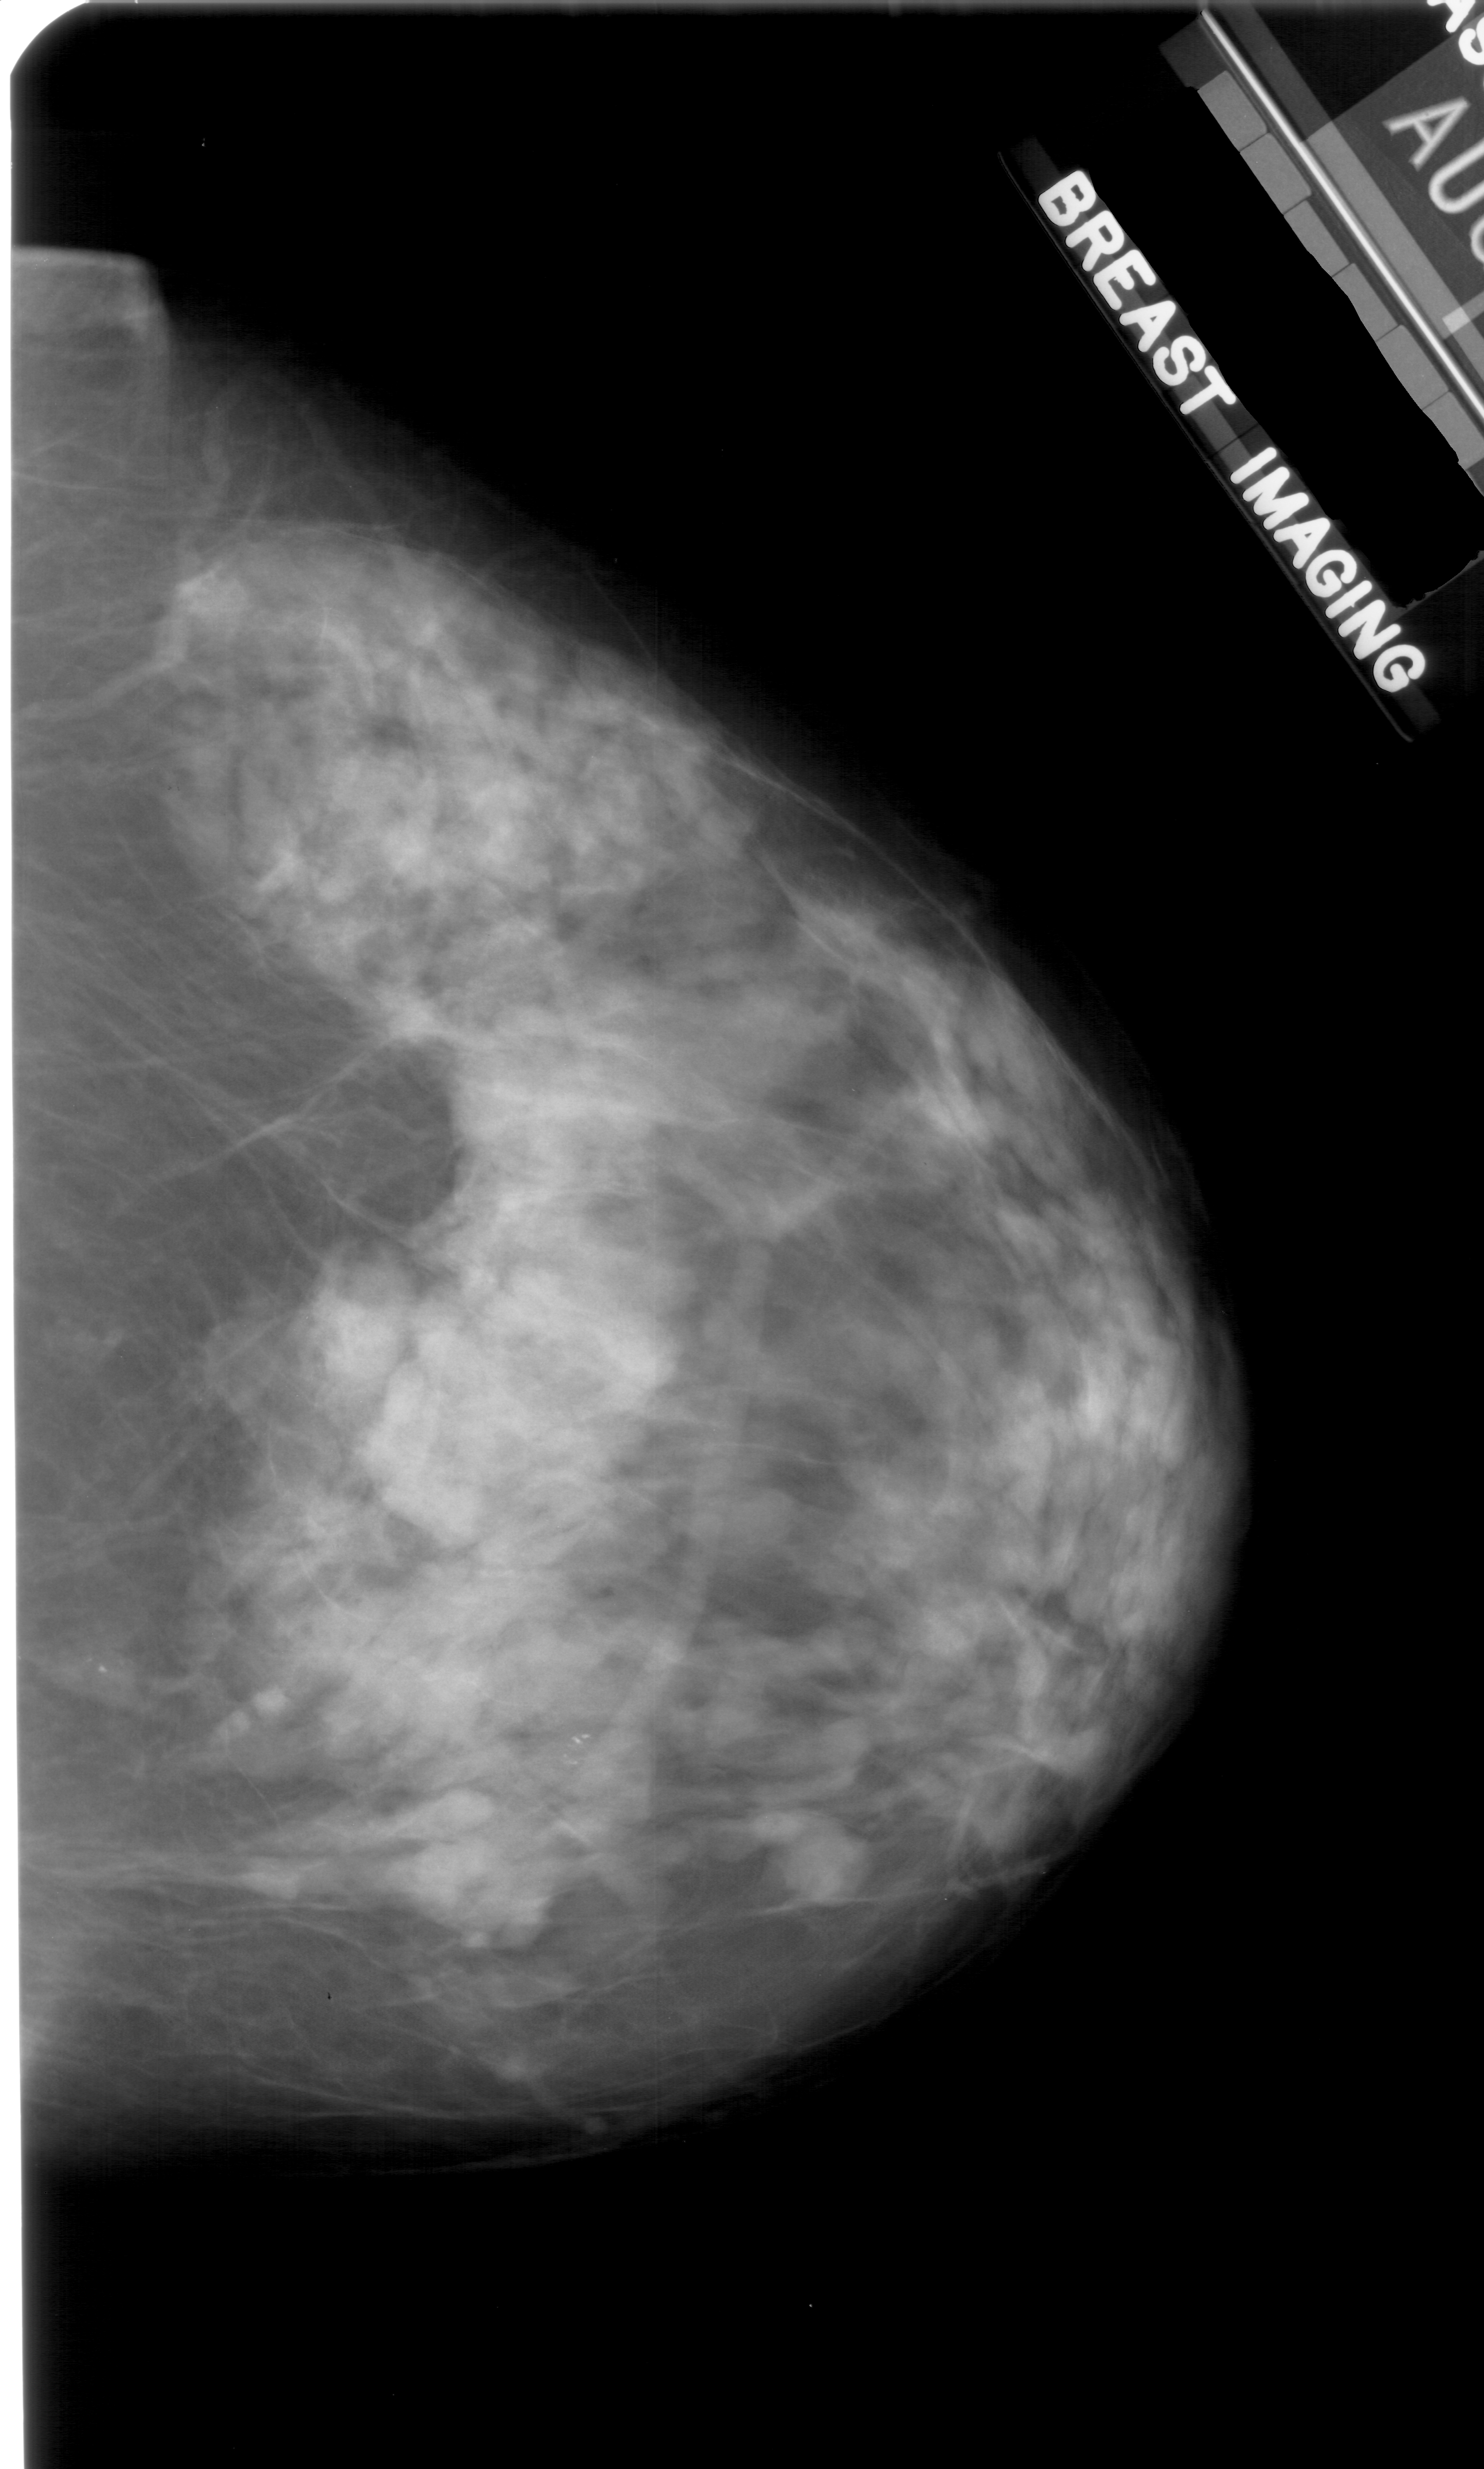
Scanned film-screen mammogram, right breast, CC view, BI-RADS breast density category 3 (scale 1–4).
Marked findings (only marked abnormalities are described; nothing is implied about the rest of the image): calcifications, morphology pleomorphic, distribution clustered; BI-RADS assessment category 4; subtlety rating 4 on a 1 (subtle) to 5 (obvious) scale; pathology result (as recorded, not read from the image): benign.